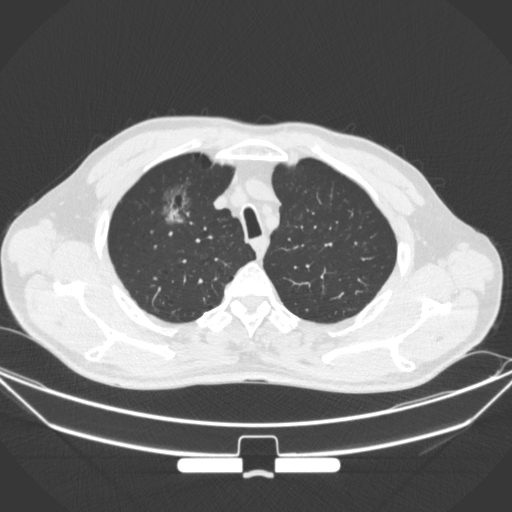
Chest CT, one axial slice; position 284 of 355 along the scan axis; lung window (W 1500 / L -600 HU); 1 mm slice thickness; 512 × 512 image matrix, field of view 399 × 399 mm. Male patient, age 67 years. From the clinical record (not read from this slice): clinical TNM (as recorded): T1c N0 M0.
Outlined on this slice (rectangle marked by the reading radiologist):
- lung tumour (recorded histology: adenocarcinoma): box from (x=151, y=175) to (x=198, y=235) px